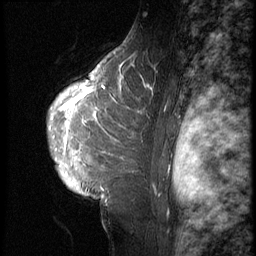
Breast MRI (dynamic contrast-enhanced), one sagittal slice; slice 44 of 62 in the series (ordered by position); 3 images stored at this slice position (order not interpretable as contrast timing); 1.5 T; TE 4.2 ms, TR 9 ms; 2.5 mm slice thickness; 256 × 256 image matrix, field of view 180 × 180 mm. Female patient, age 28 years. From the clinical record (not read from this slice): setting: breast cancer imaged before/during neoadjuvant chemotherapy.
Outlined on this slice (semi-automatic segmentation, software-assisted and operator-edited):
- analysis volume of interest (the breast-tissue region the enhancement analysis was run in; not a lesion): bounding box (x1, y1, x2, y2) in pixels: (46, 45, 192, 207)
- tumour enhancement mask (voxels above the 140 % enhancement threshold inside the analysis volume of interest): (60, 63, 192, 187)